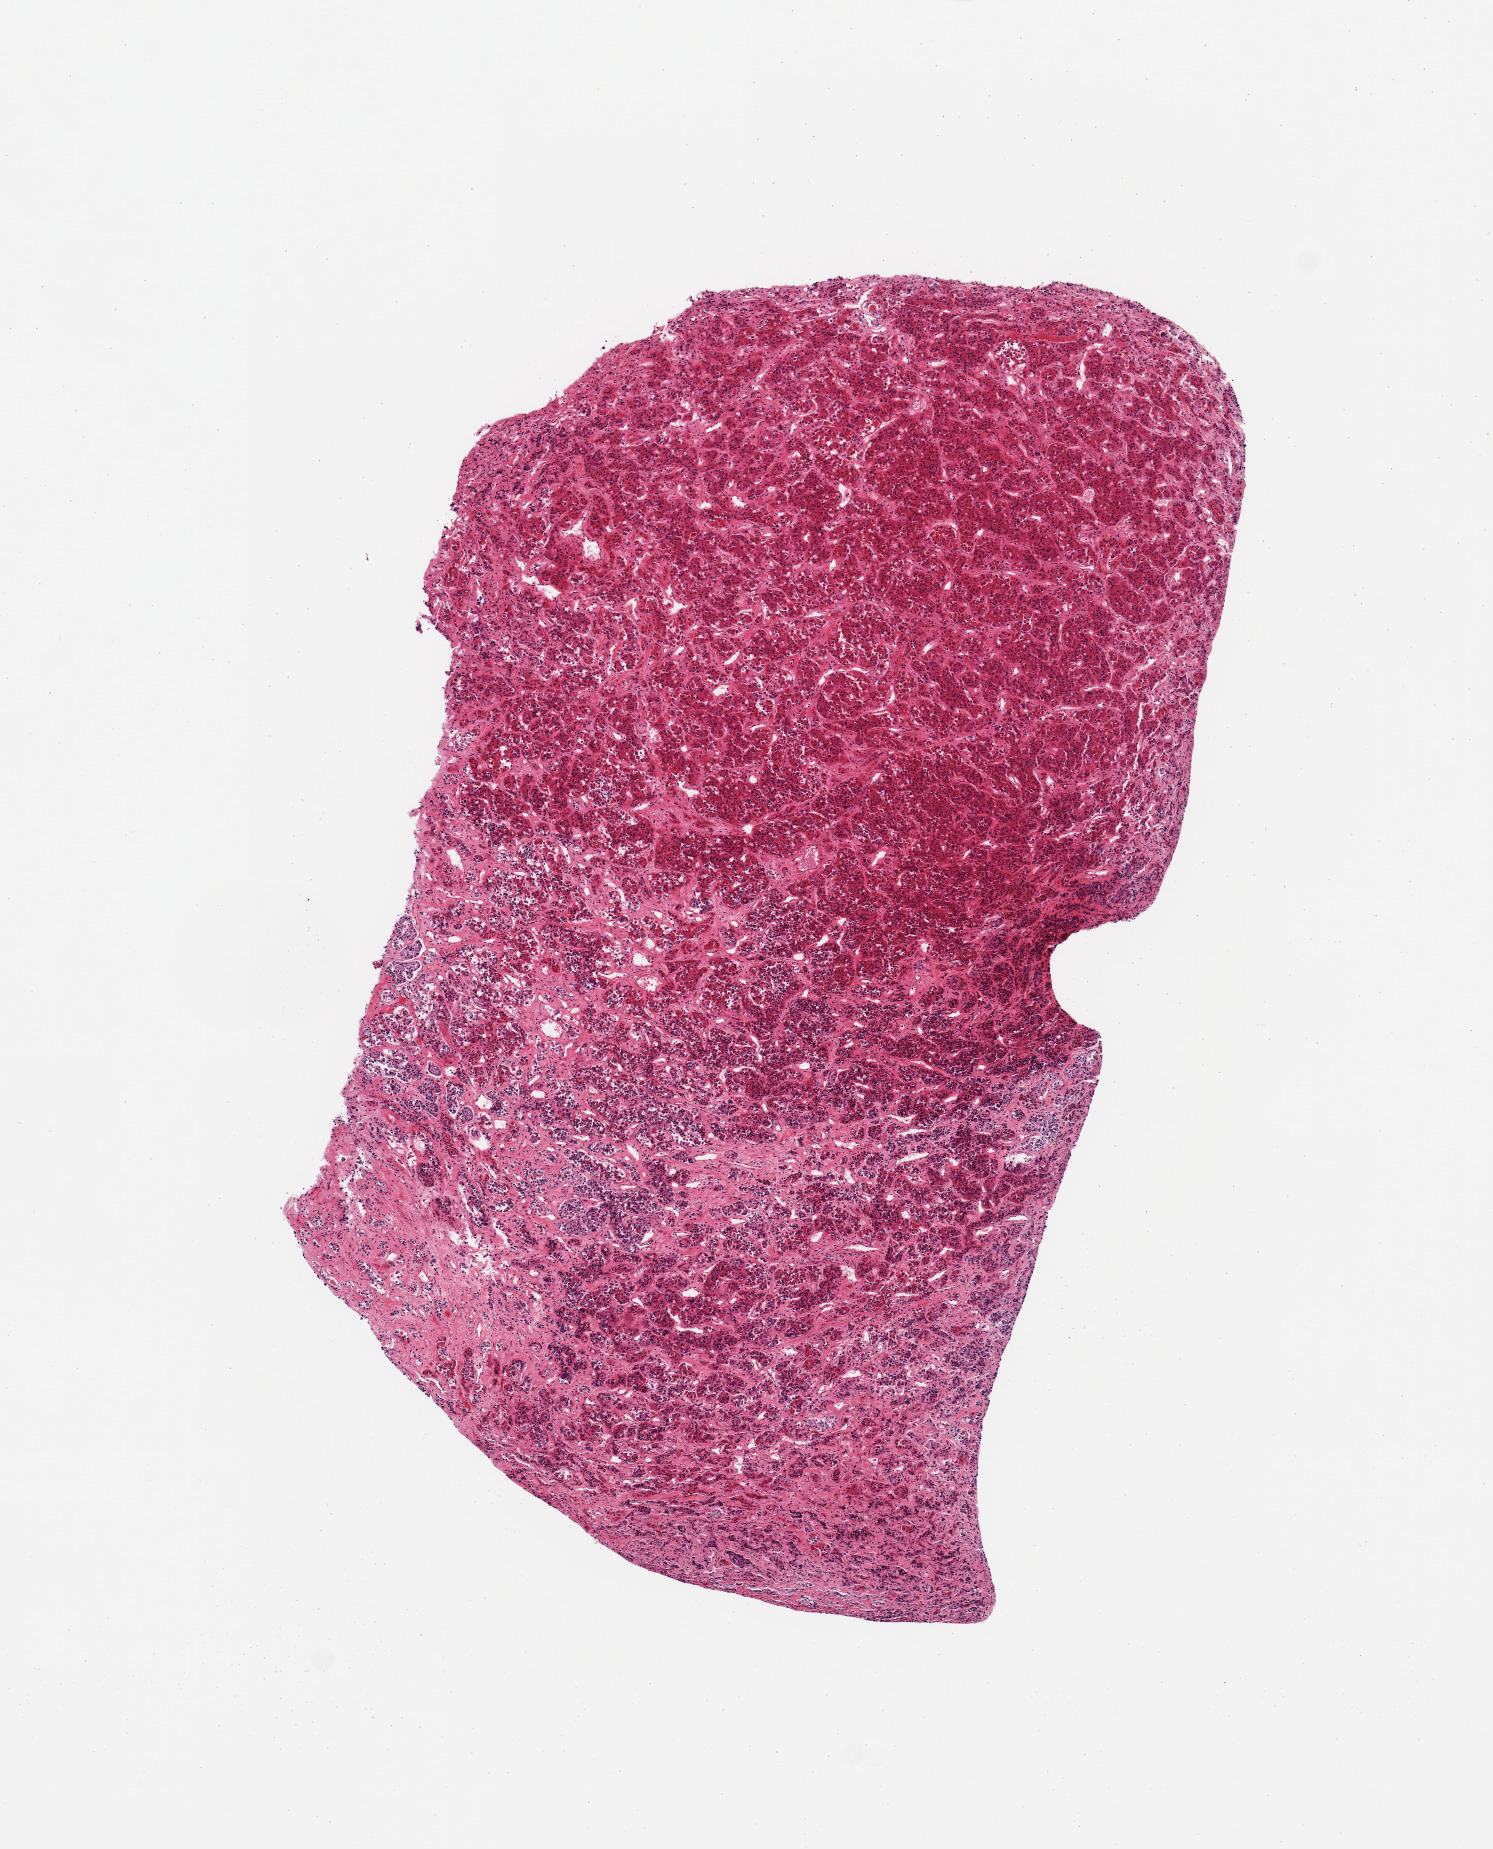
H&E whole-slide image — whole scanned area (about 5.9 x 7.3 mm) shown as a low-resolution overview, PAXgene-fixed, paraffin-embedded tissue, target tissue: pituitary, donor tissue sample. Donor sex: male.
Pathologist's review note for this sample: 1 piece, adenohypophysis.